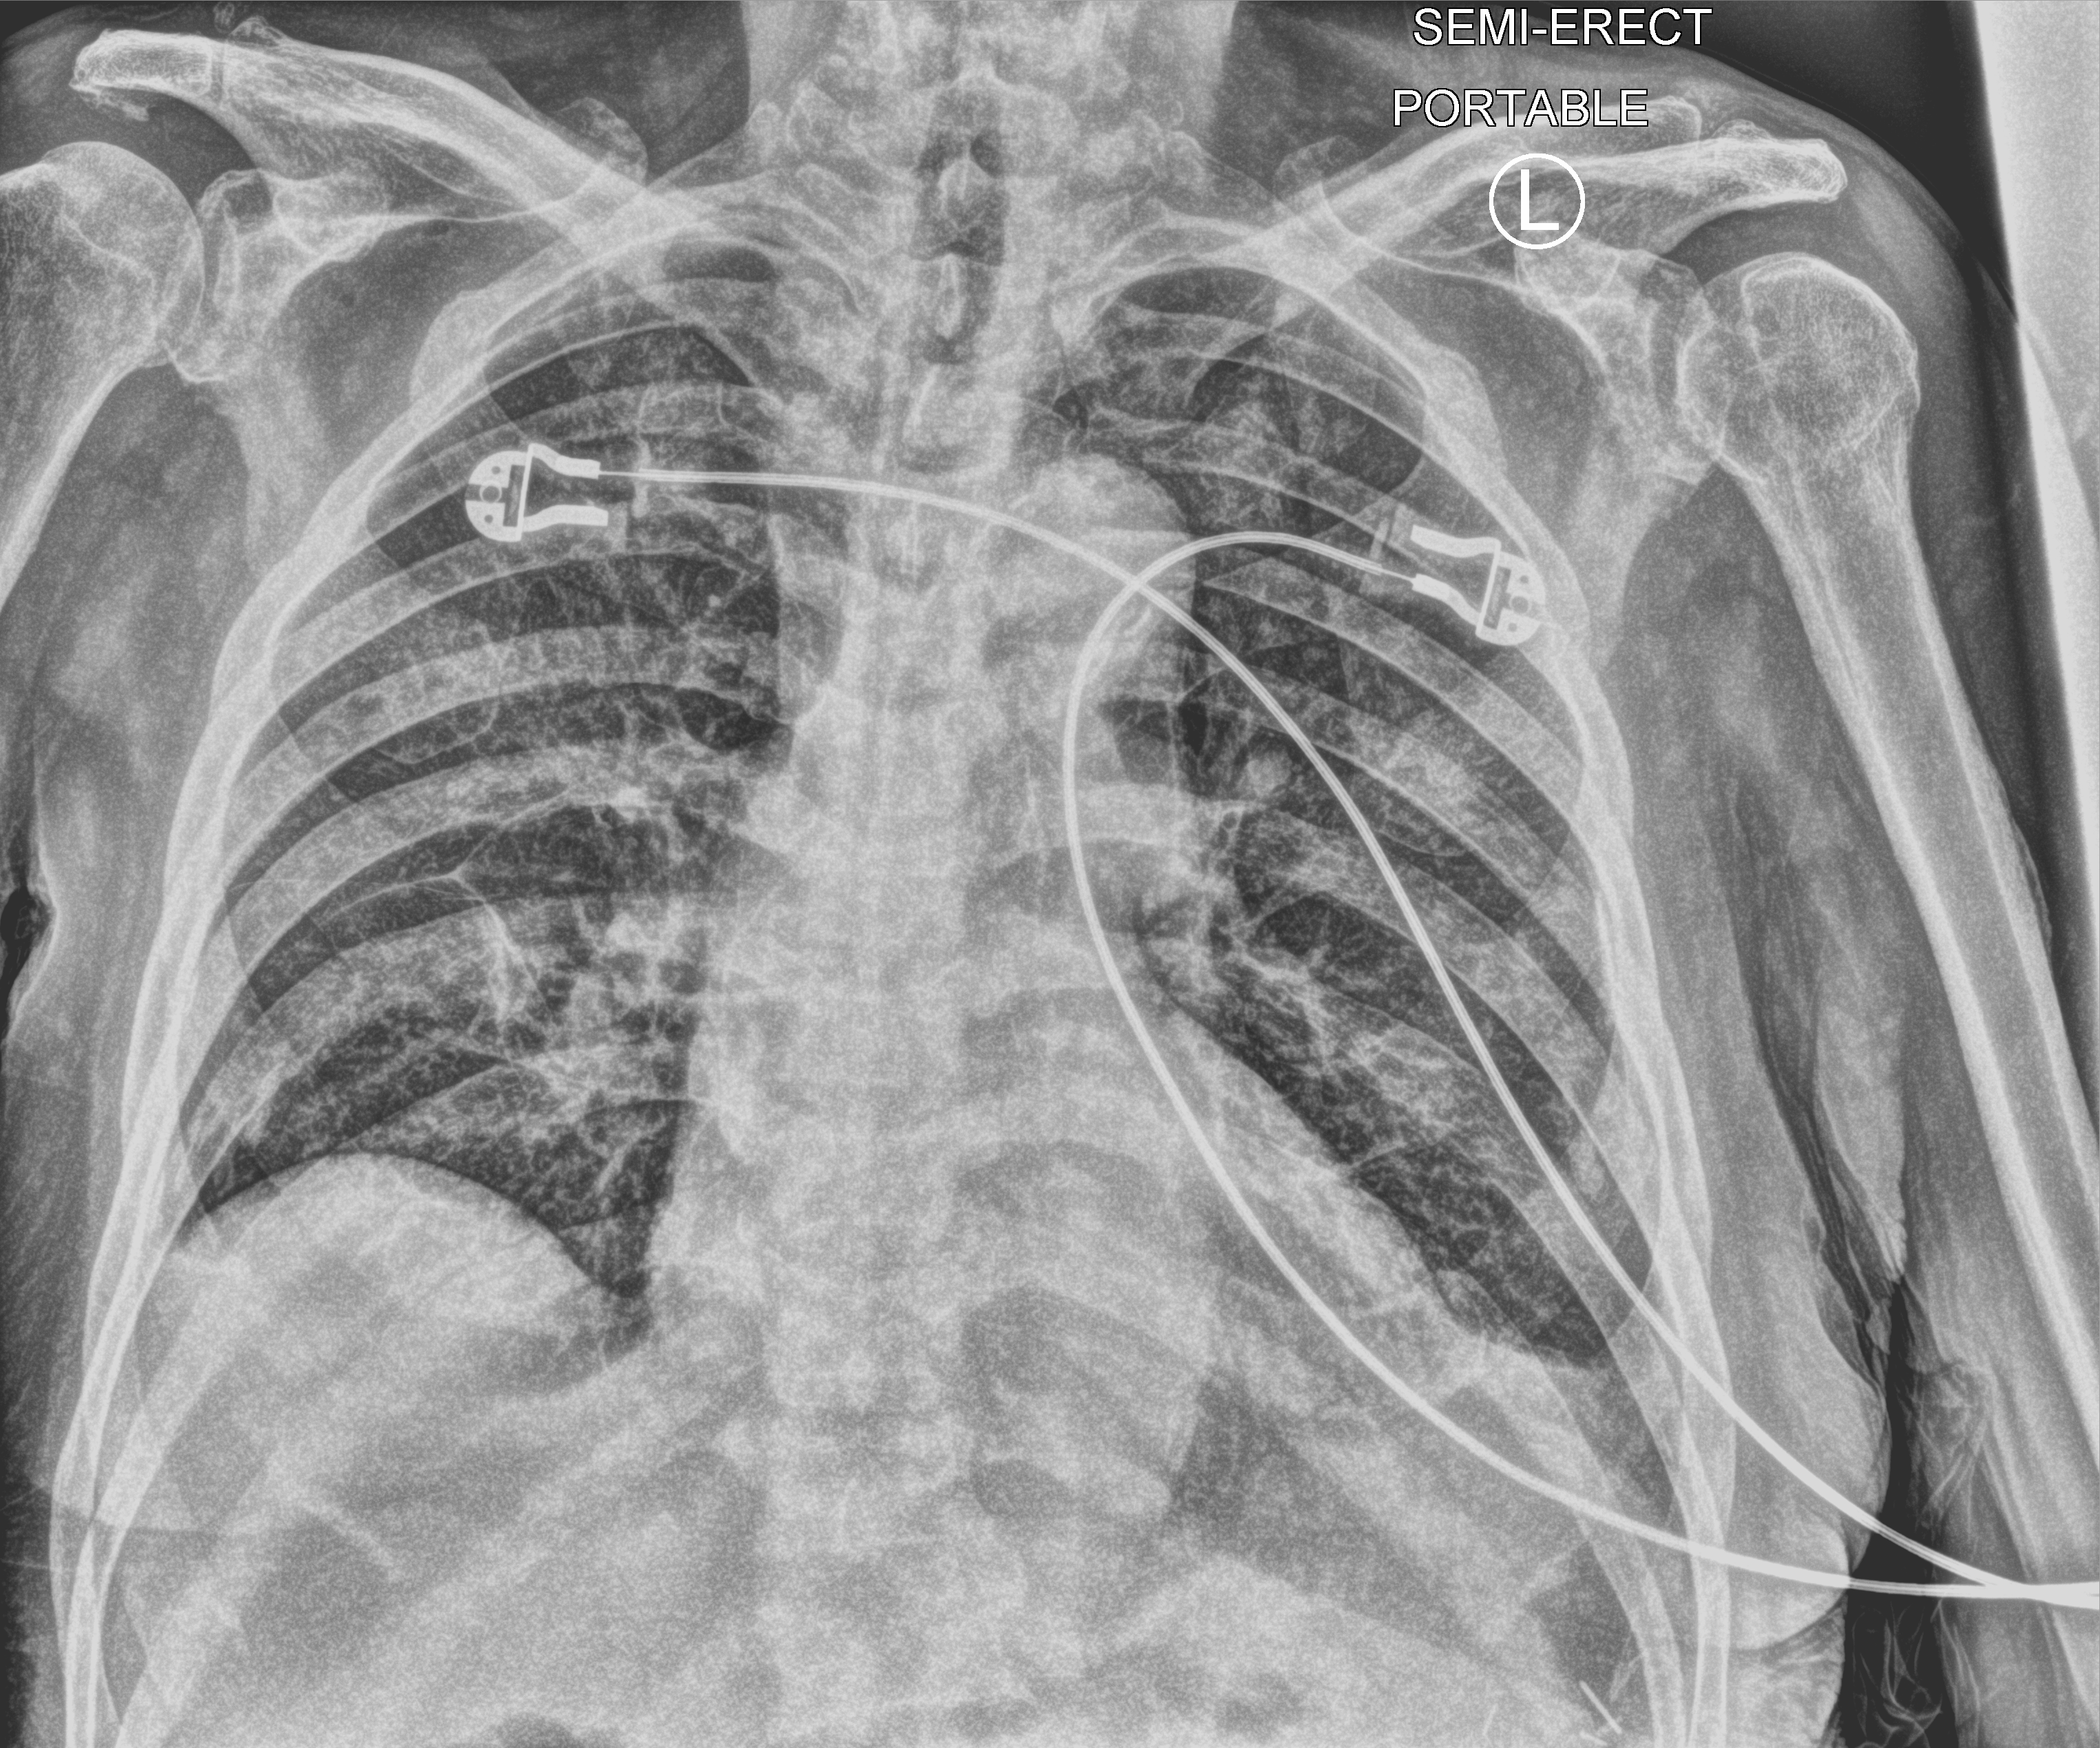
Portable chest radiograph, anteroposterior (AP) projection. Male patient hospitalised with COVID-19, age 75–90 years.
Hospital-stay facts (about this admission, not read from this image; timing relative to this image not recorded):
- admitted to intensive care during this hospital stay: no
- length of hospital stay: 12 days
- mechanically ventilated during this hospital stay: no